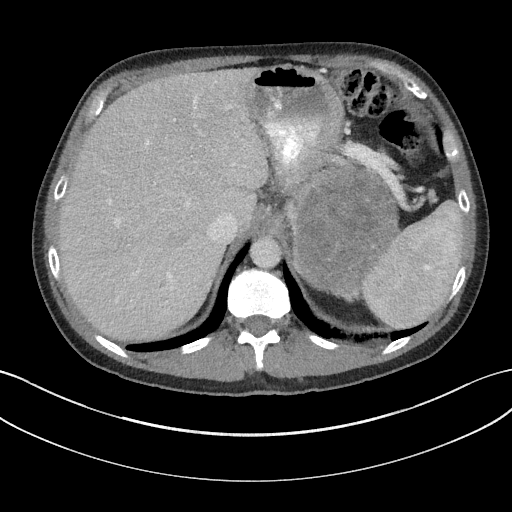
Contrast-enhanced abdominal CT, one axial slice. Position 126 of 147 along the scan axis. Reconstruction kernel I31f/3. Intravenous contrast given. Soft-tissue window (W 400 / L 40 HU). 3 mm slice thickness. 512 × 512 image matrix. Male patient, age 58 years. From the clinical record (not read from this slice): diagnosis: adrenocortical carcinoma; tumour side: left adrenal; tumour size at pathology: 22 cm; Ki-67 index: 26 %; stage (as recorded): 2.
Annotated regions visible in this slice (semi-automatic segmentation, software-assisted and operator-edited):
- mass: bounding box <292,169,398,294> (left, top, right, bottom; pixels)